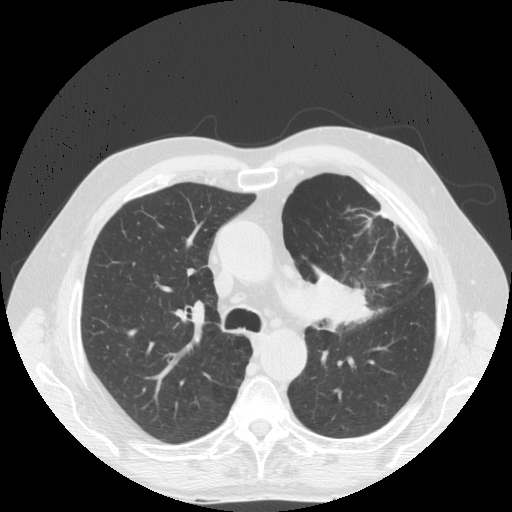
Low-dose screening chest CT, axial slice. Baseline screening round. Lung window (W 1500 / L -600 HU). Slice 54 of 171 in the series. 512 × 512 image matrix. Male participant, aged 70 years at enrolment.
Lesion marked by an expert reader, bounding box [x1, y1, x2, y2] px = [293, 255, 386, 344]. The exam's reader record, not a measurement of the box and not confirmed to be the same lesion: non-calcified nodule or mass ≥4 mm, left upper lobe, 46 × 31 mm, spiculated (stellate) margins, soft tissue attenuation. Participant outcome: lung cancer diagnosed 78 days after this screen — squamous cell carcinoma, NOS, left upper lobe, poorly differentiated (G3), stage IIIB (AJCC 6th edition), 46 mm at pathology.